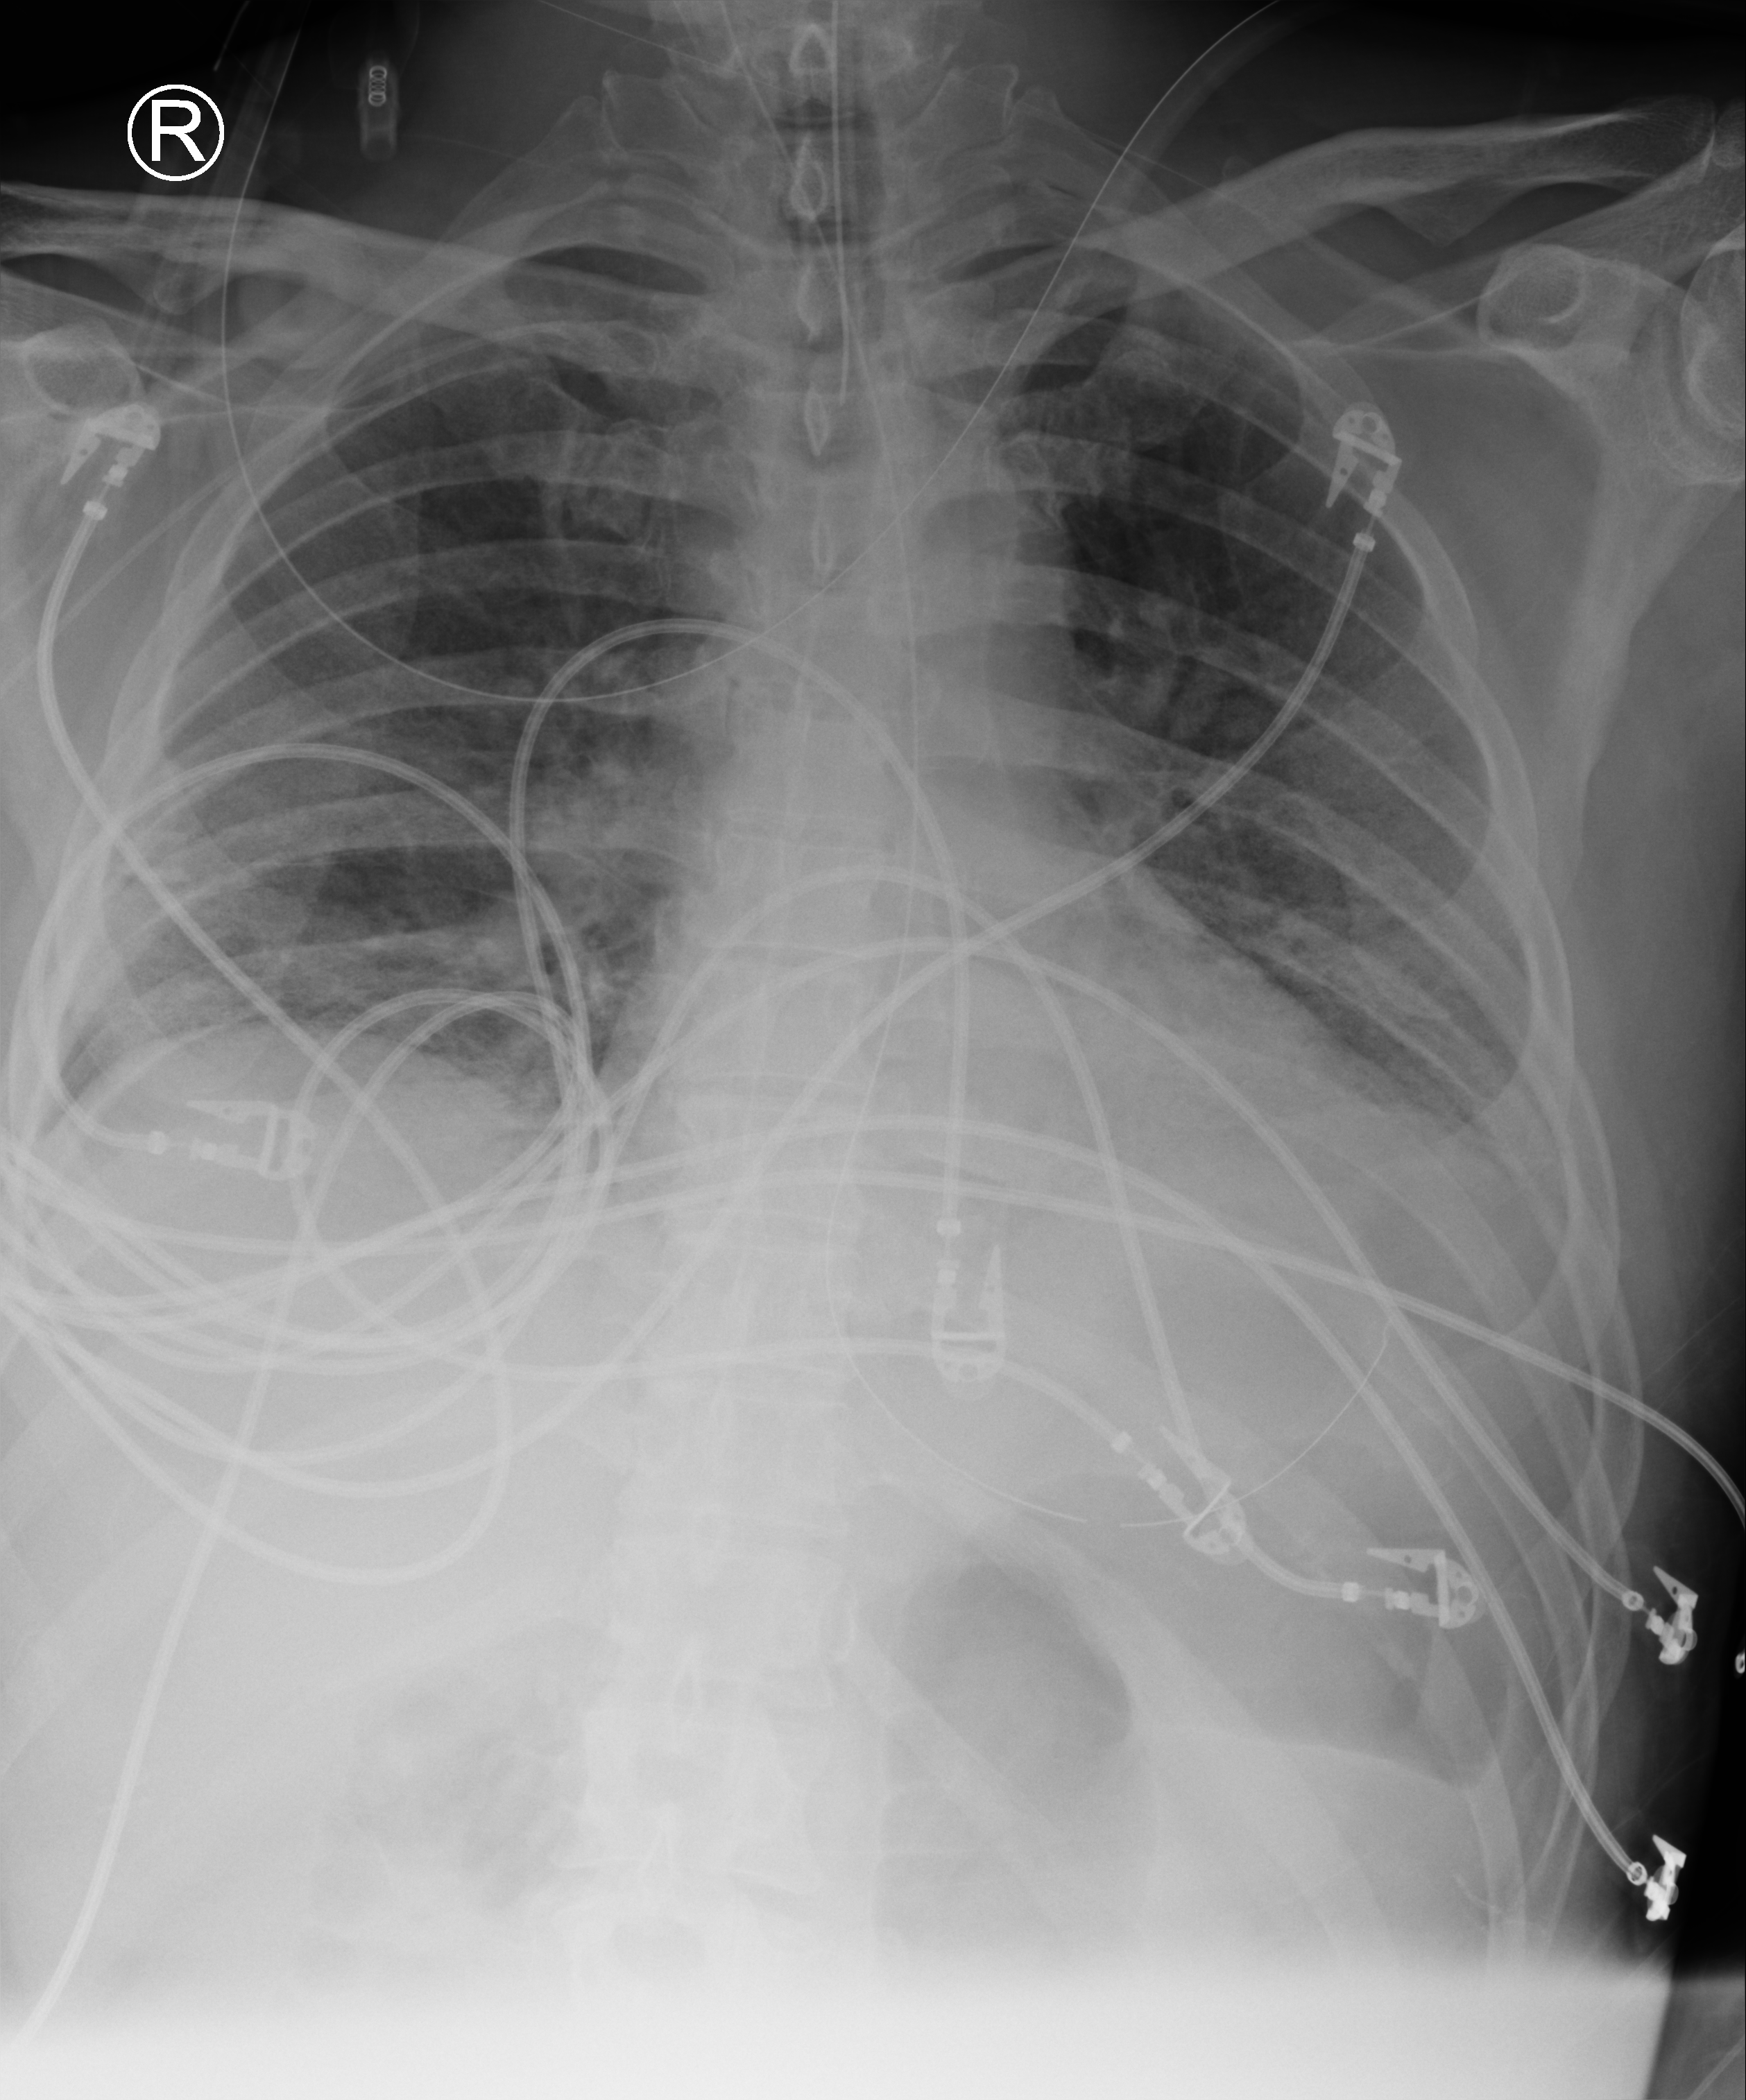
Portable chest radiograph; anteroposterior (AP) projection. Male patient hospitalised with COVID-19, age 60–74 years.
From the hospital-stay record, not from the radiograph (when in the stay this image was taken is not recorded): mechanically ventilated during this hospital stay: yes; length of hospital stay: 26 days.